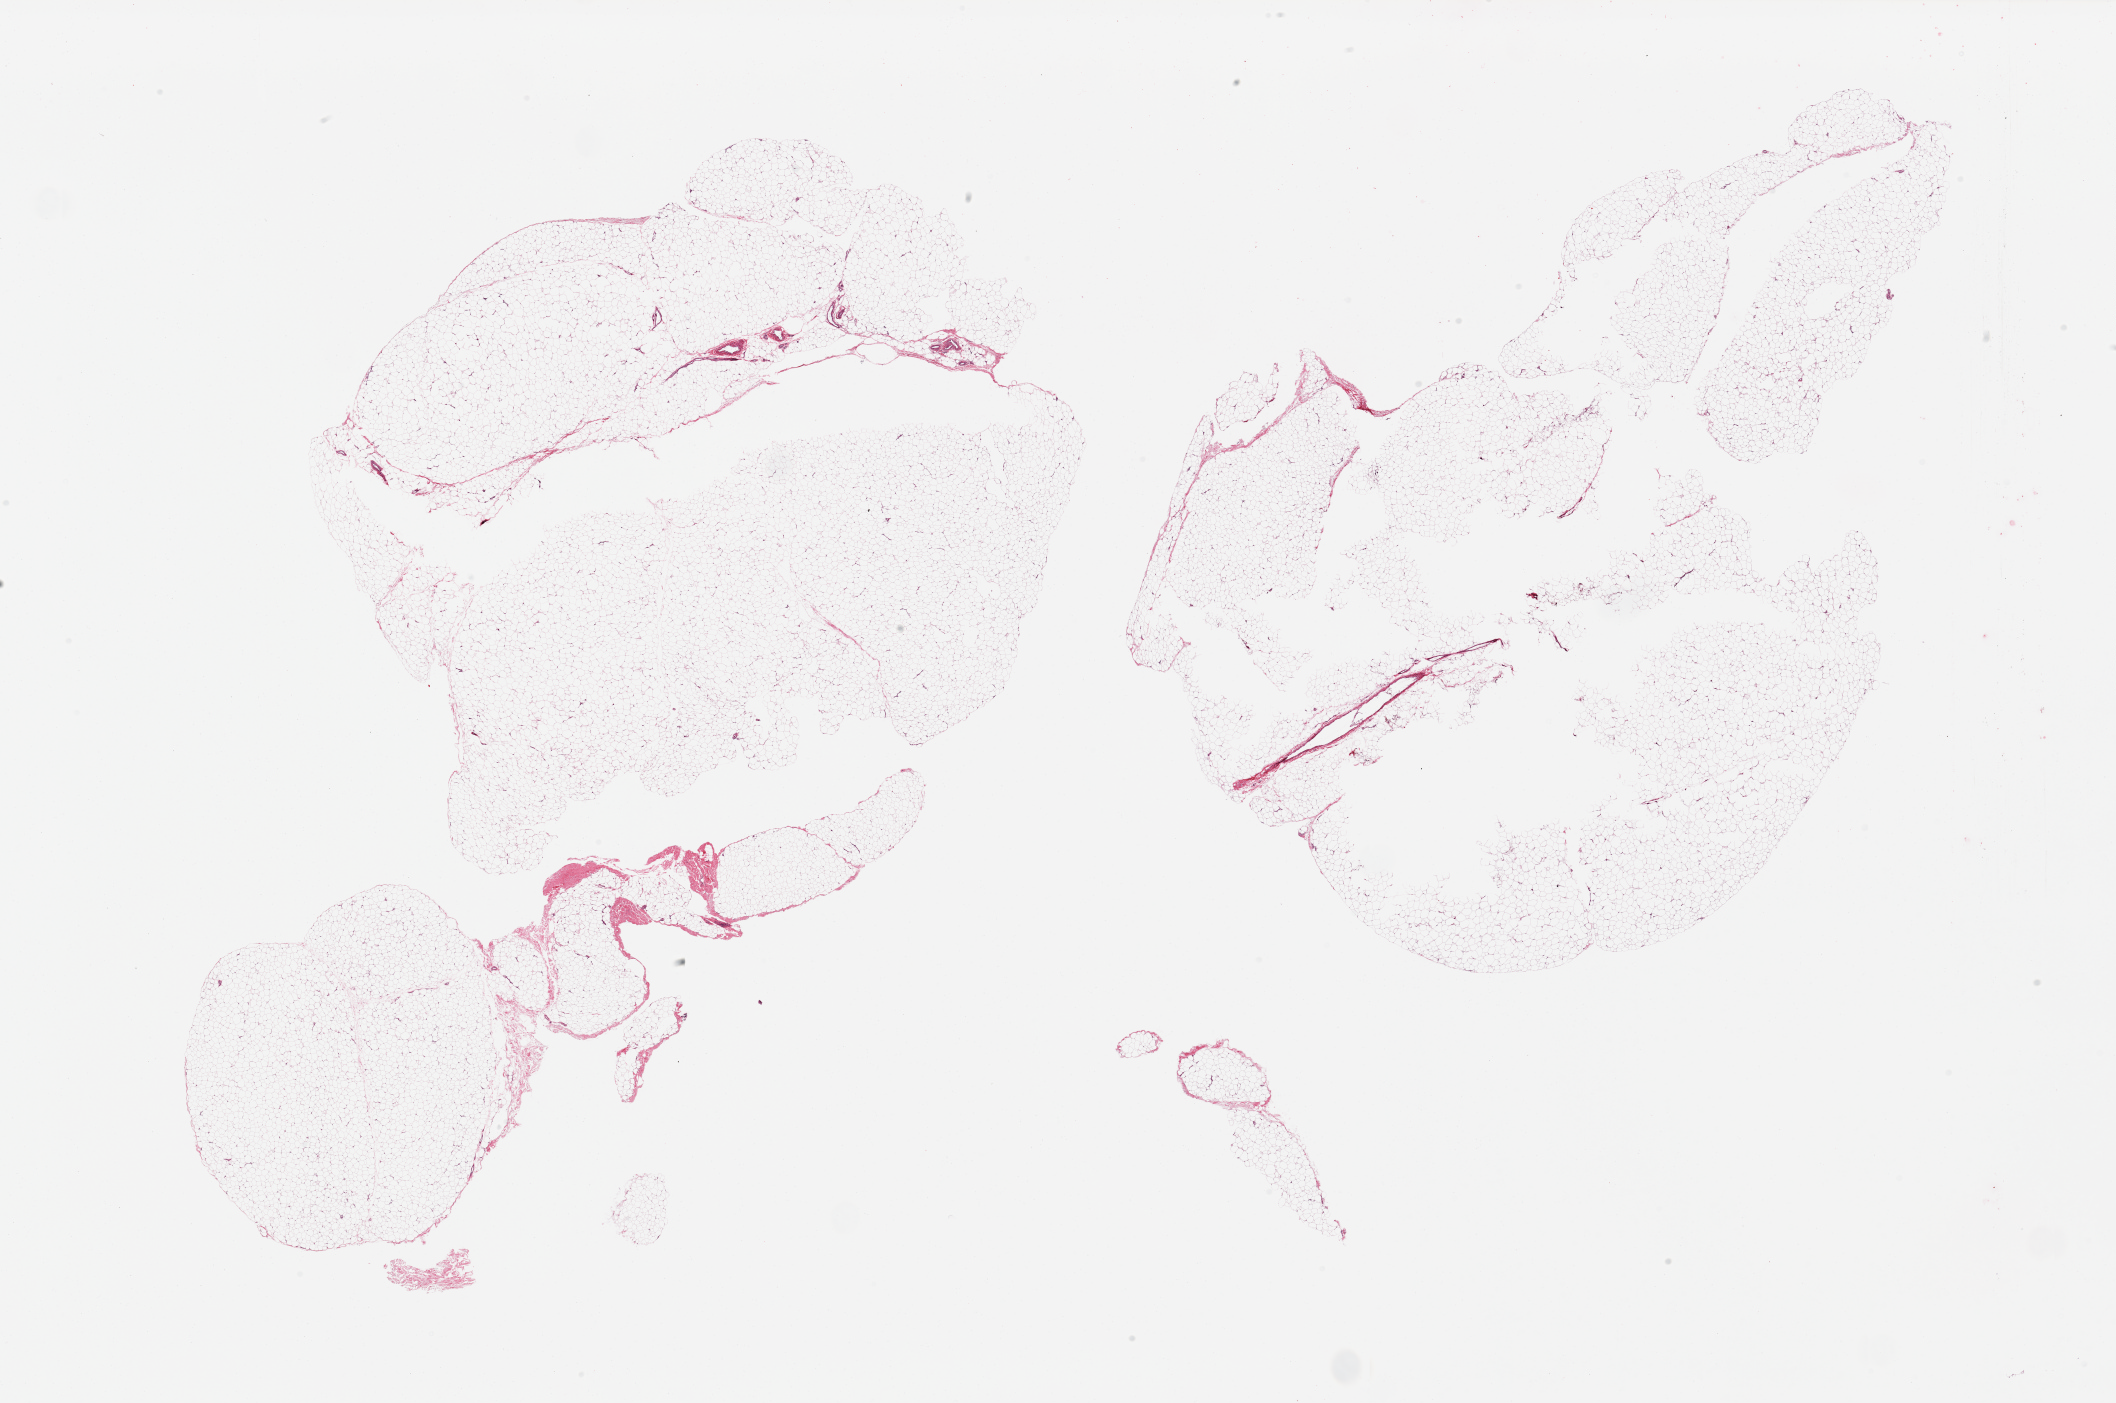
Digitized hematoxylin and eosin (H&E)-stained section — whole scanned area (about 33.5 x 22.2 mm, acquisition: 20x scan) shown as a low-resolution overview, PAXgene-fixed, paraffin-embedded tissue, target tissue: adipose tissue, donor tissue sample. Donor: male.
Reviewer comment on this tissue sample: 2 pieces.